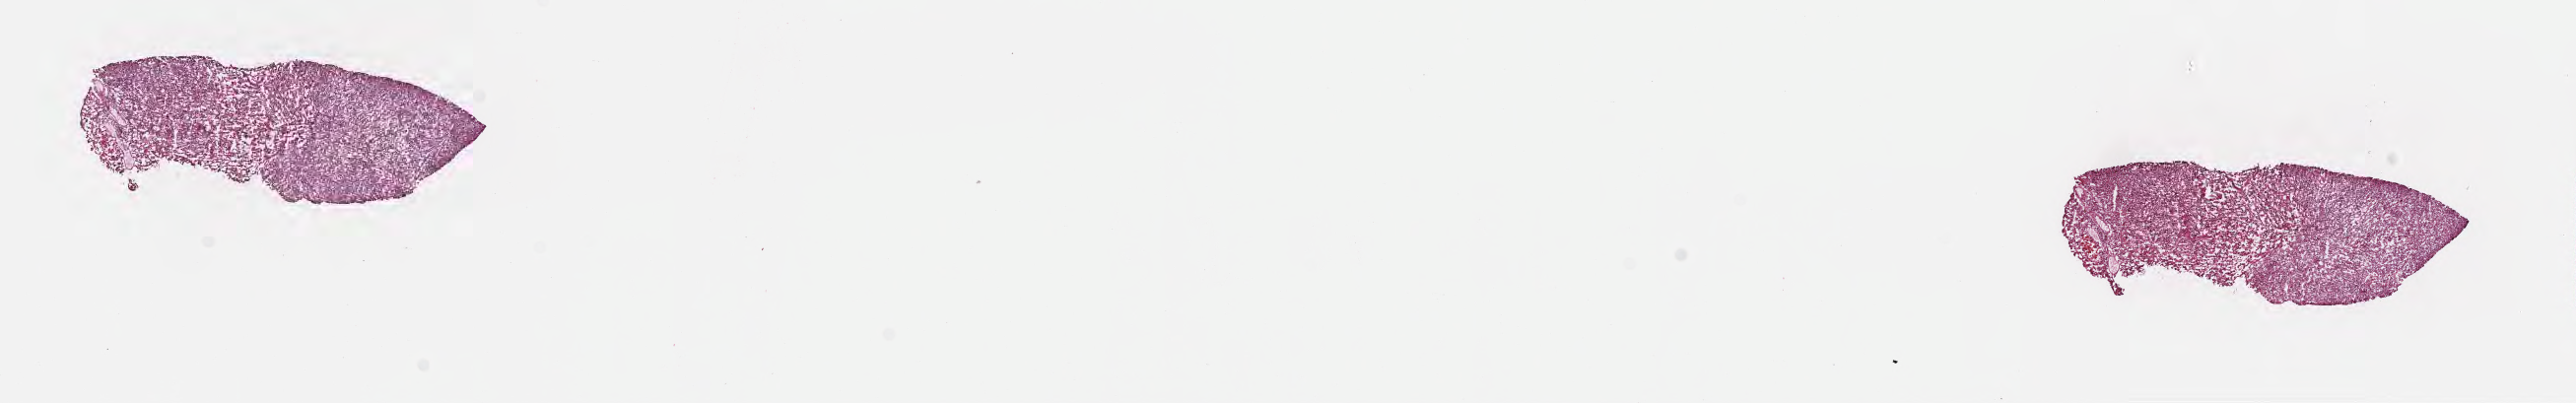
Hematoxylin and eosin (H&E) whole-slide image — whole scanned area (about 21.1 x 3.3 mm) shown as a low-resolution overview; frozen section; specimen: metastatic tumor tissue, resected from brain. Patient: female, age at initial diagnosis 74 years. Composition of this section per pathologist review: tumor cells 88%, tumor nuclei 97%, stromal cells 10%, necrosis 2%, normal cells 0%. Inflammatory infiltration, as recorded: lymphocyte infiltration 2%, monocyte infiltration 0%, neutrophil infiltration 0%.
* patient diagnosis (primary): Malignant melanoma, NOS